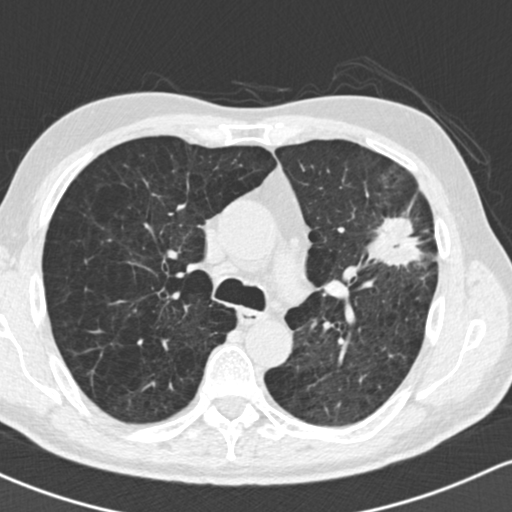
Low-dose screening chest CT, one axial slice; position 101 of 162 along the scan axis; lung window (W 1500 / L -600 HU); 2 mm slice thickness; 512 × 512 image matrix.
Structures marked on this image (manually delineated by an expert):
- lesion 1 (tumor, upper lobe of left lung): bounding box [x1, y1, x2, y2] px = [367, 213, 424, 267]